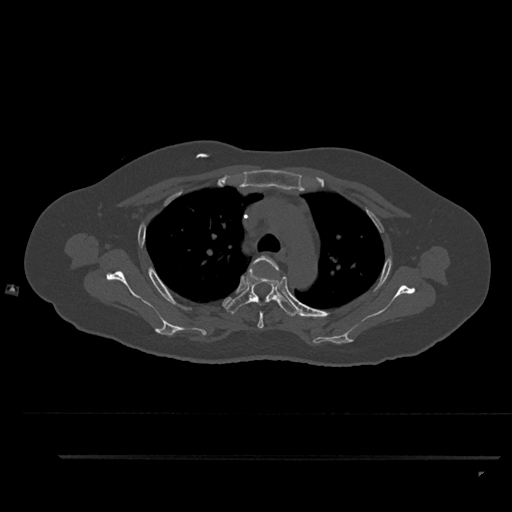
CT including the spine, one axial slice; 120 kVp; bone window (W 1800 / L 400 HU); 0.5 mm slice thickness; 512 × 512 image matrix, field of view 408 × 408 mm. Patient: female, 44 years. Case-level facts recorded for this patient, not image findings: primary cancer: renal; vertebrae with lytic lesions (as recorded): L1.
Structures marked on this image (semi-automatically segmented with operator editing):
- T3 vertebra: bounding box (x1, y1, x2, y2) in pixels: (250, 255, 280, 329)
- T4 vertebra: (226, 267, 299, 317)